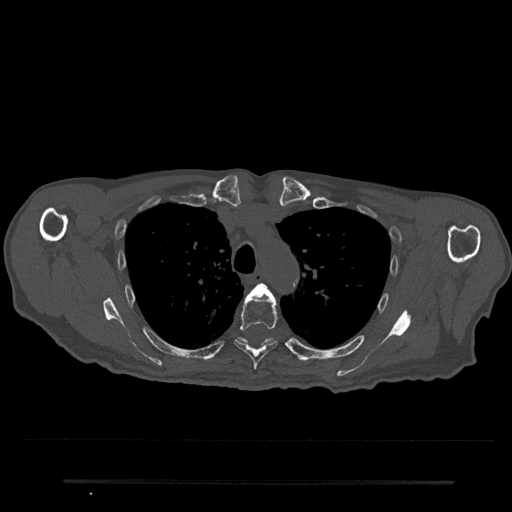
CT including the spine, one axial slice. Position 575 of 797 along the scan axis. Reconstruction kernel Br40s/3. Bone window (W 1800 / L 400 HU). 0.5 mm slice thickness. 512 × 512 image matrix, field of view 427 × 427 mm. Patient: male, 74 years. Case-level facts recorded for this patient, not image findings: primary cancer: prostate.
Annotated regions visible in this slice (semi-automatic segmentation, software-assisted and operator-edited):
- T4 vertebra: box from (x=250, y=283) to (x=272, y=296) px
- T5 vertebra: (x=234, y=292)–(x=278, y=370)
- T6 vertebra: (x=237, y=338)–(x=295, y=355)